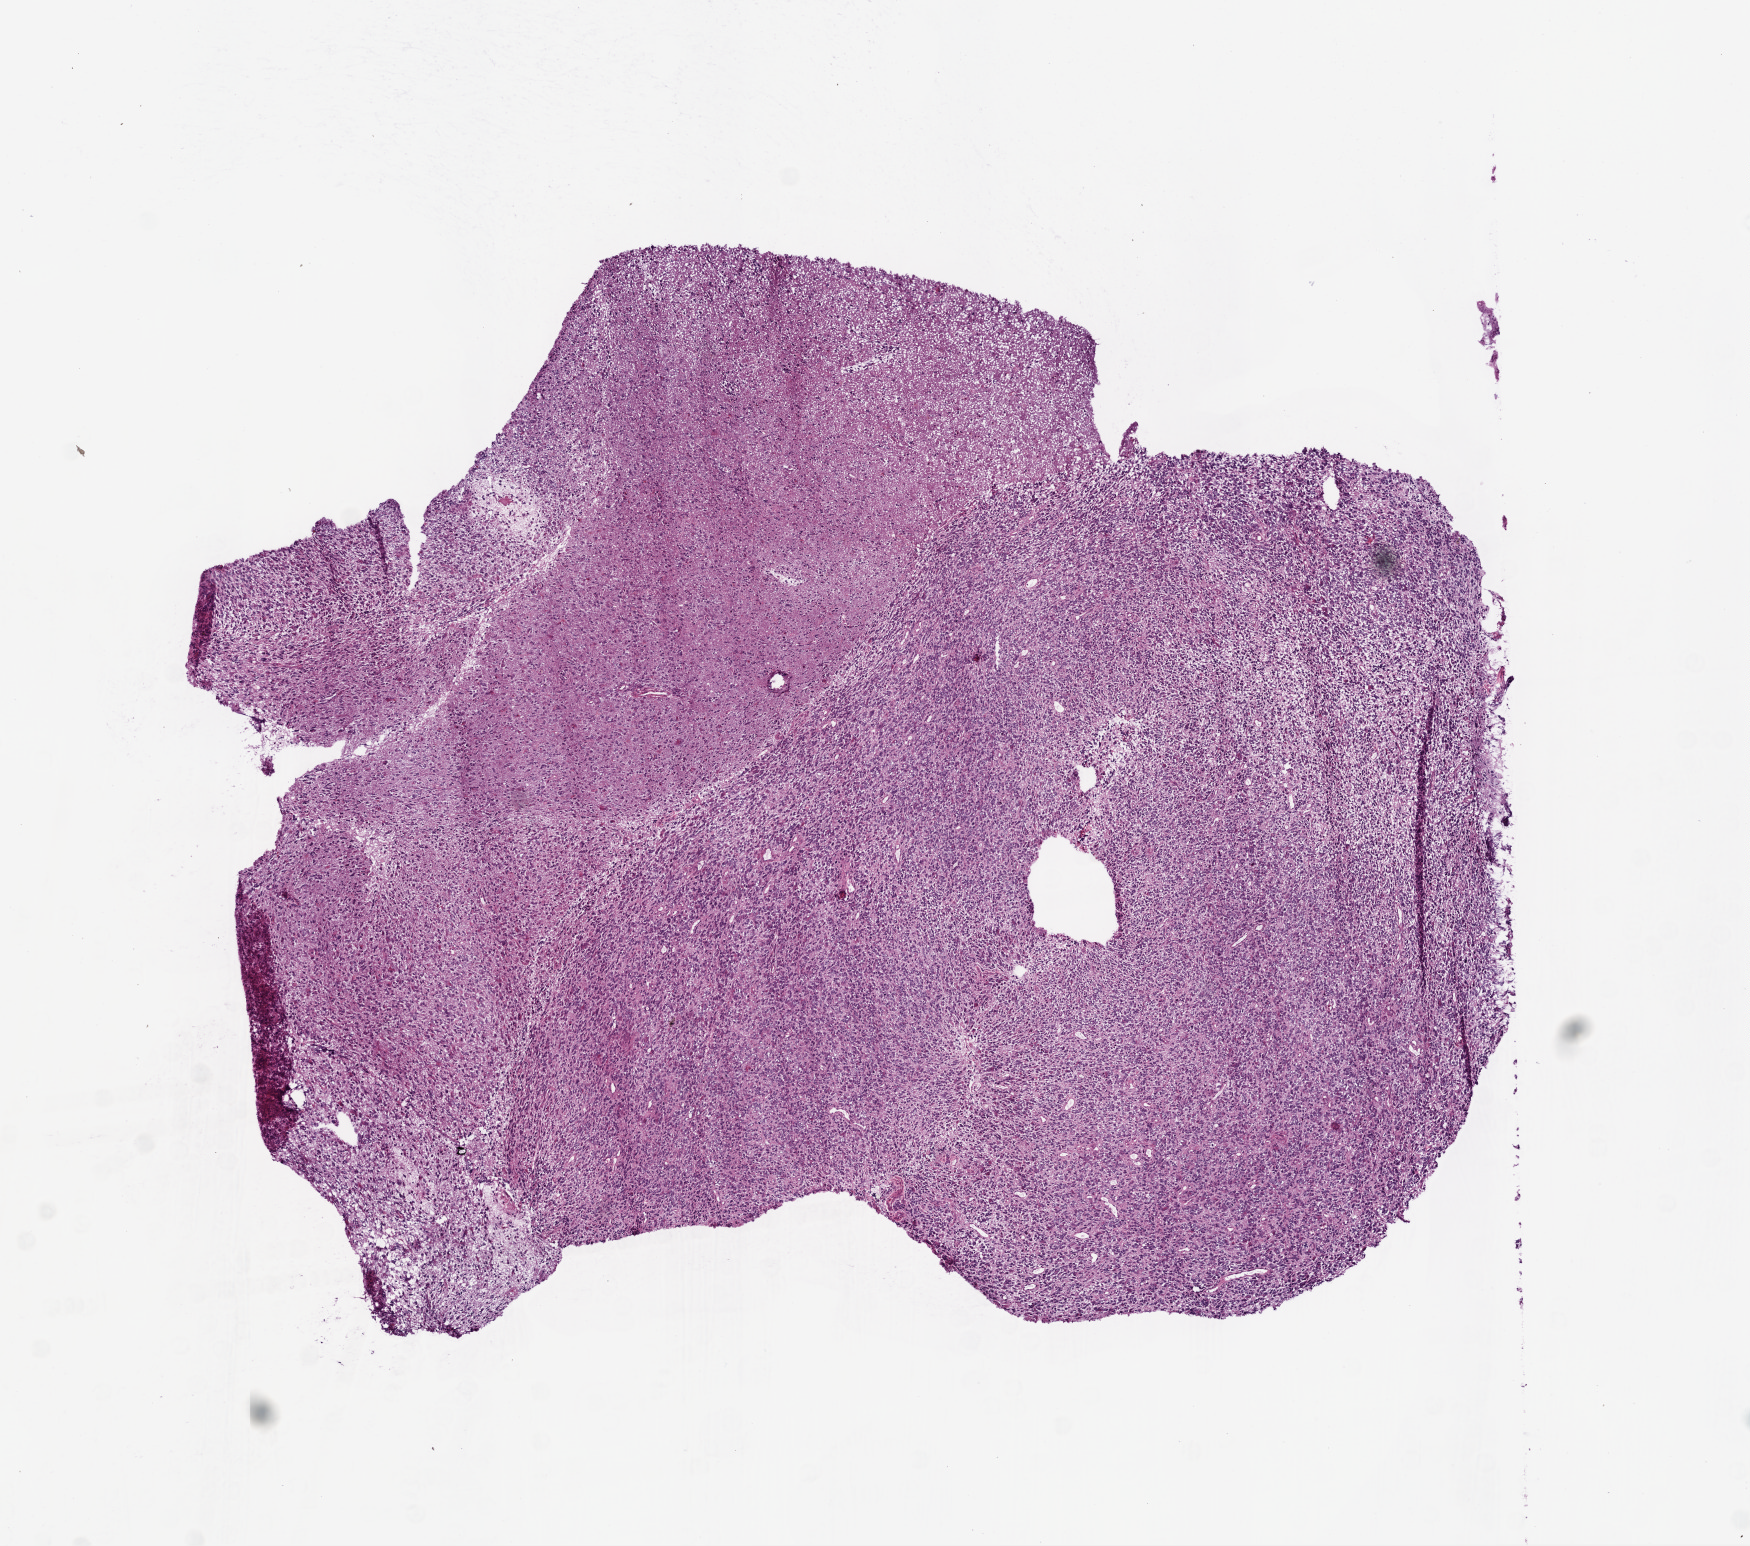
Hematoxylin and eosin (H&E) stained whole-slide image, whole scanned area (about 7.0 x 6.2 mm) shown as a low-resolution overview; frozen section from the top of the tissue portion; primary tumour sample from the brain. Male patient; age at initial diagnosis 73 years. Composition of this section per pathologist review: tumour cells 98%, tumour nuclei 85%, normal cells 0%, stromal cells 0%, necrosis 2%.
Histologic diagnosis: Glioblastoma.